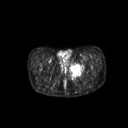
FDG PET of an extremity soft-tissue mass (from a PET/CT study), one axial slice; slice 41 of 267 in the series (ordered by position); 3.27 mm slice thickness; 128 × 128 image matrix. Male patient, age 59 years. From the clinical record (not read from this slice): histological type: pleiomorphic liposarcoma; grade: high; site of the primary tumour: left thigh.
Structures marked on this image (expert contour drawn on MRI and transferred to this co-registered scan by the dataset authors):
- gross tumour volume including surrounding oedema: box from (x=70, y=63) to (x=84, y=78) px
- gross tumour volume (mass): (x=70, y=64)–(x=83, y=74)